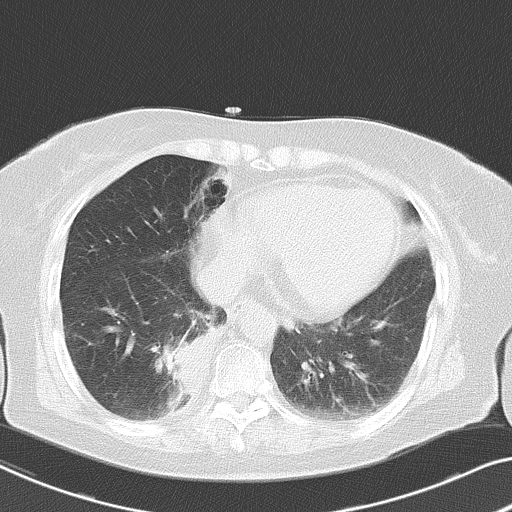
Chest CT, one axial slice; position 17 of 53 along the scan axis; reconstruction kernel B70f; 120 kVp; lung window (W 1500 / L -600 HU); 5 mm slice thickness; 512 × 512 image matrix, field of view 333 × 333 mm. Patient: female, 70 years. Case-level facts recorded for this patient, not image findings: clinical TNM (as recorded): T2 N1 M1a.
Outlined on this slice (rectangle marked by the reading radiologist):
- lung tumour (recorded histology: adenocarcinoma): bounding box (x1, y1, x2, y2) in pixels: (160, 327, 219, 401)